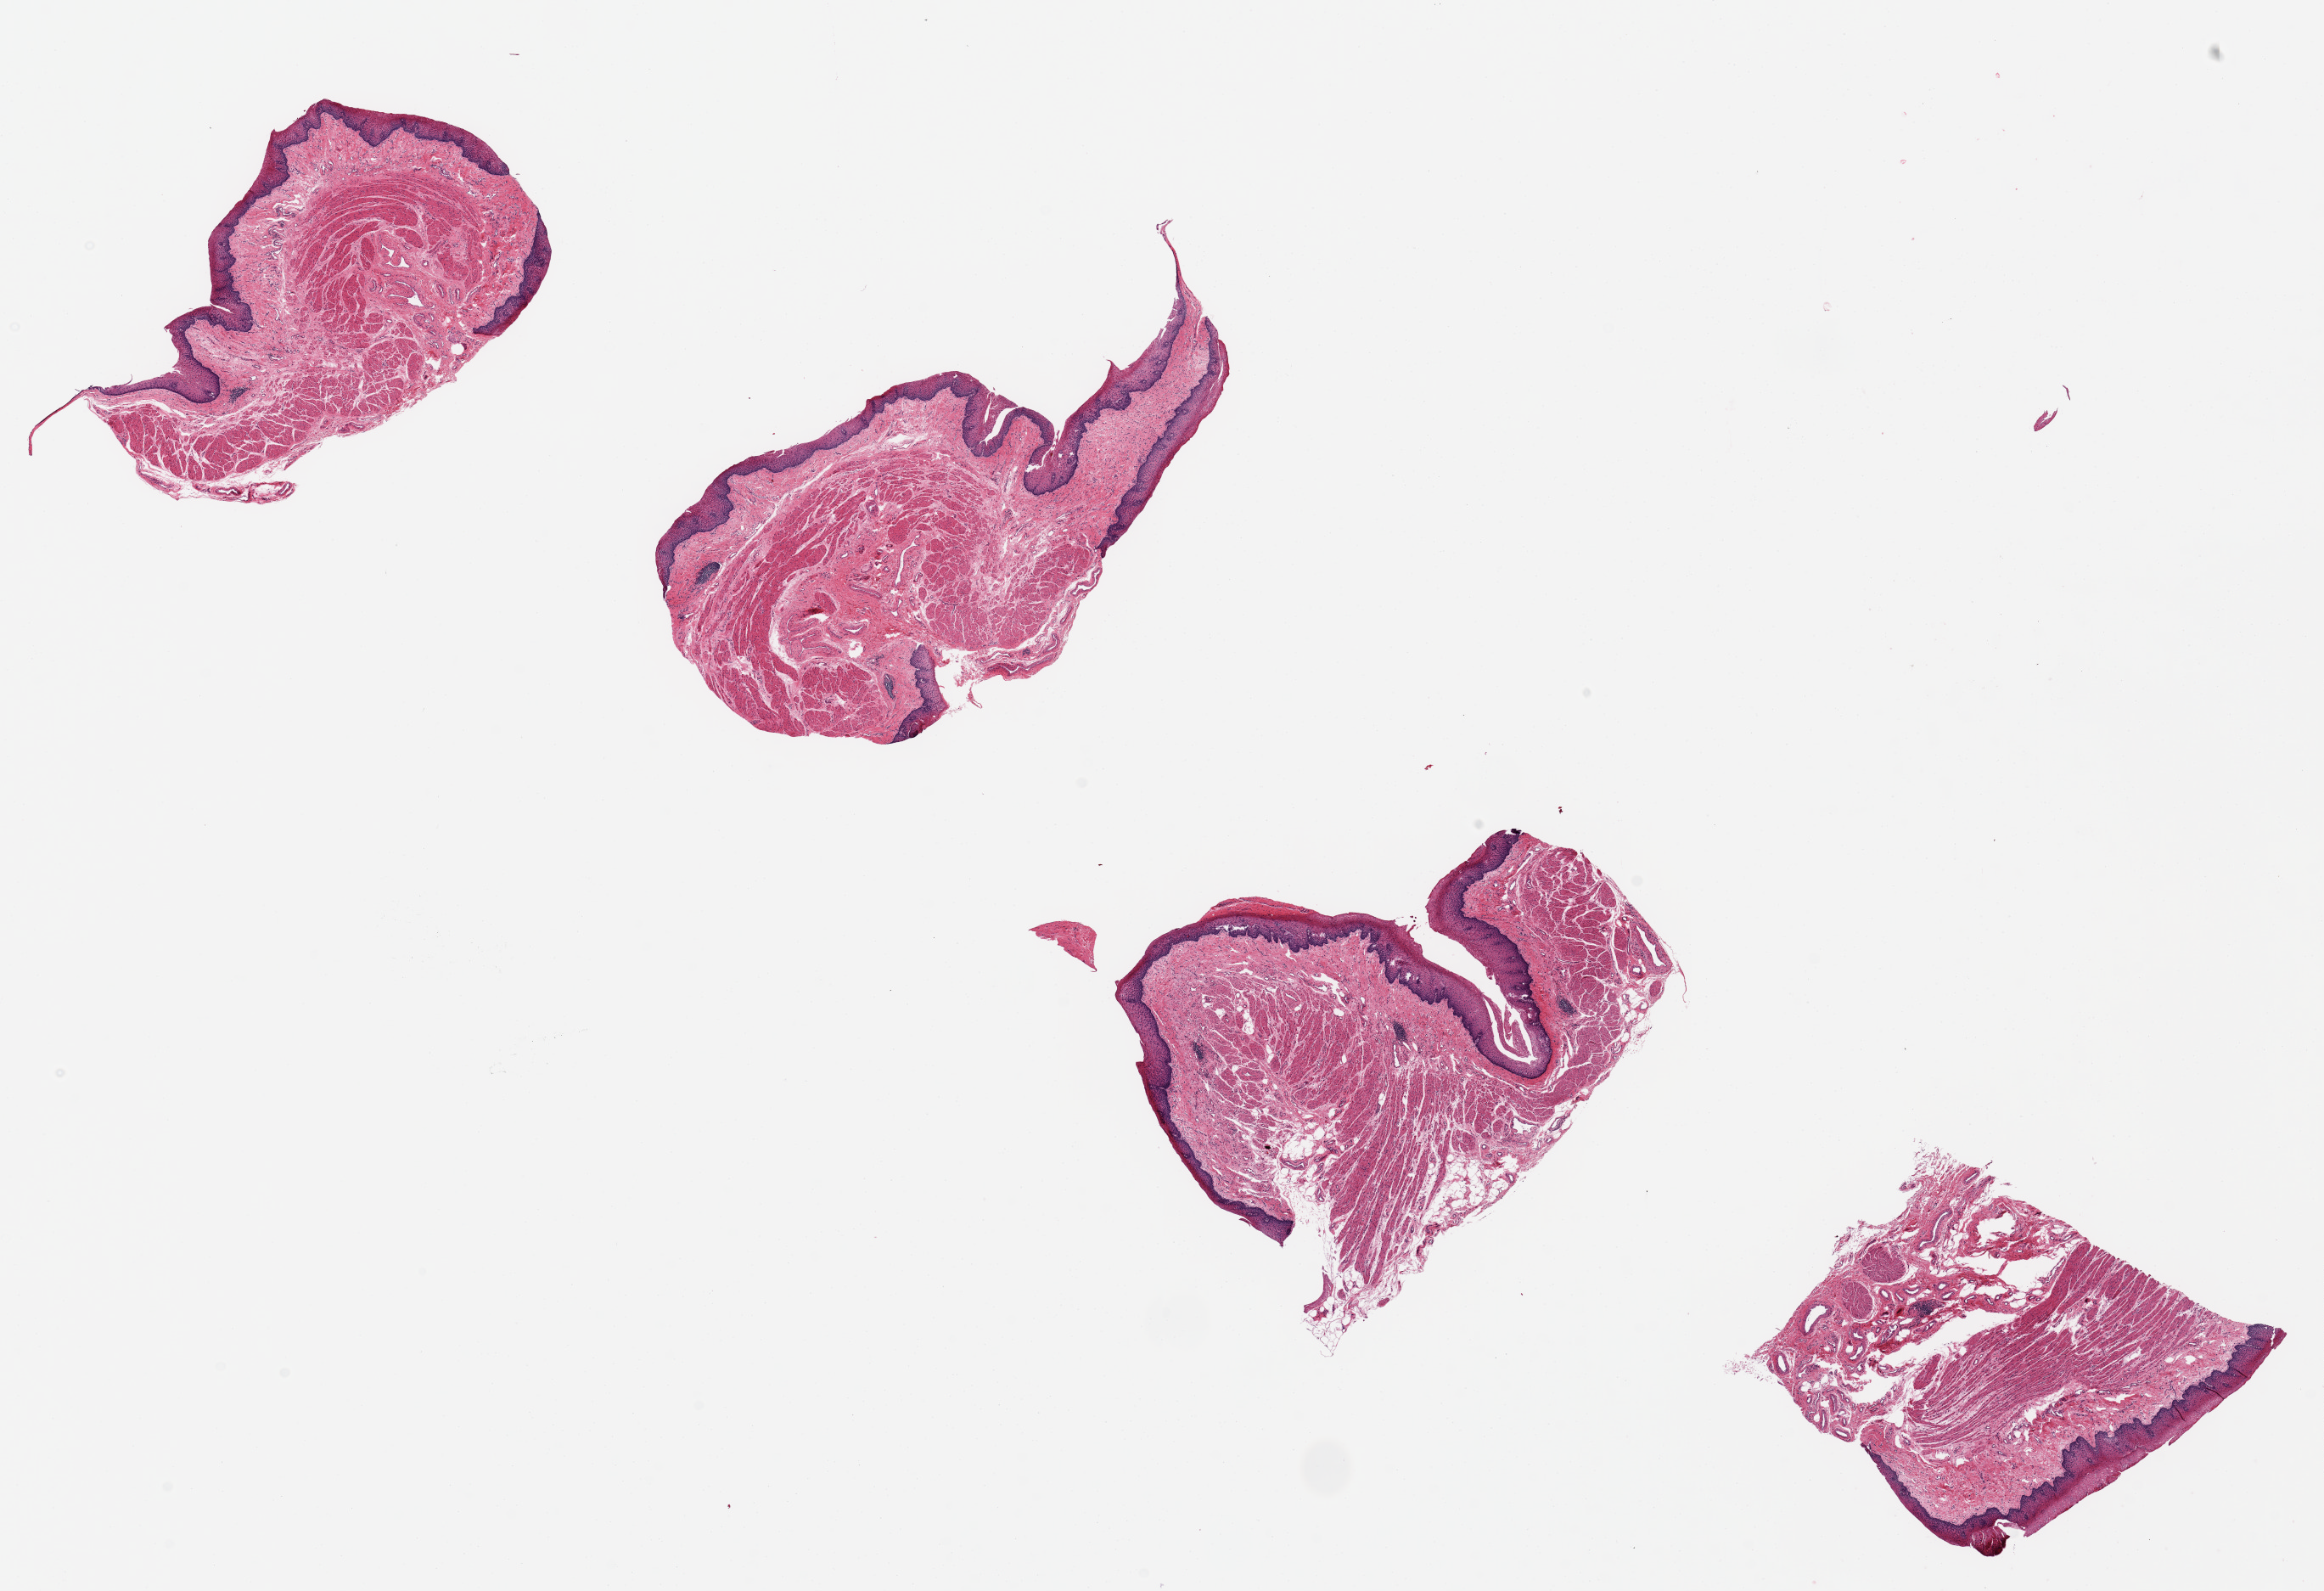
Whole-slide image, H&E stain, brightfield — whole scanned area (about 21.7 x 14.8 mm, from a 20x scan) shown as a low-resolution overview; PAXgene-fixed paraffin-embedded (PFPE) section; target tissue: esophageal mucous membrane; tissue donor sample. Donor sex: male.
• pathologist's review note for this sample: 4 ~4x3mm pieces. Squamous mucosa is ~8-10% of thickness